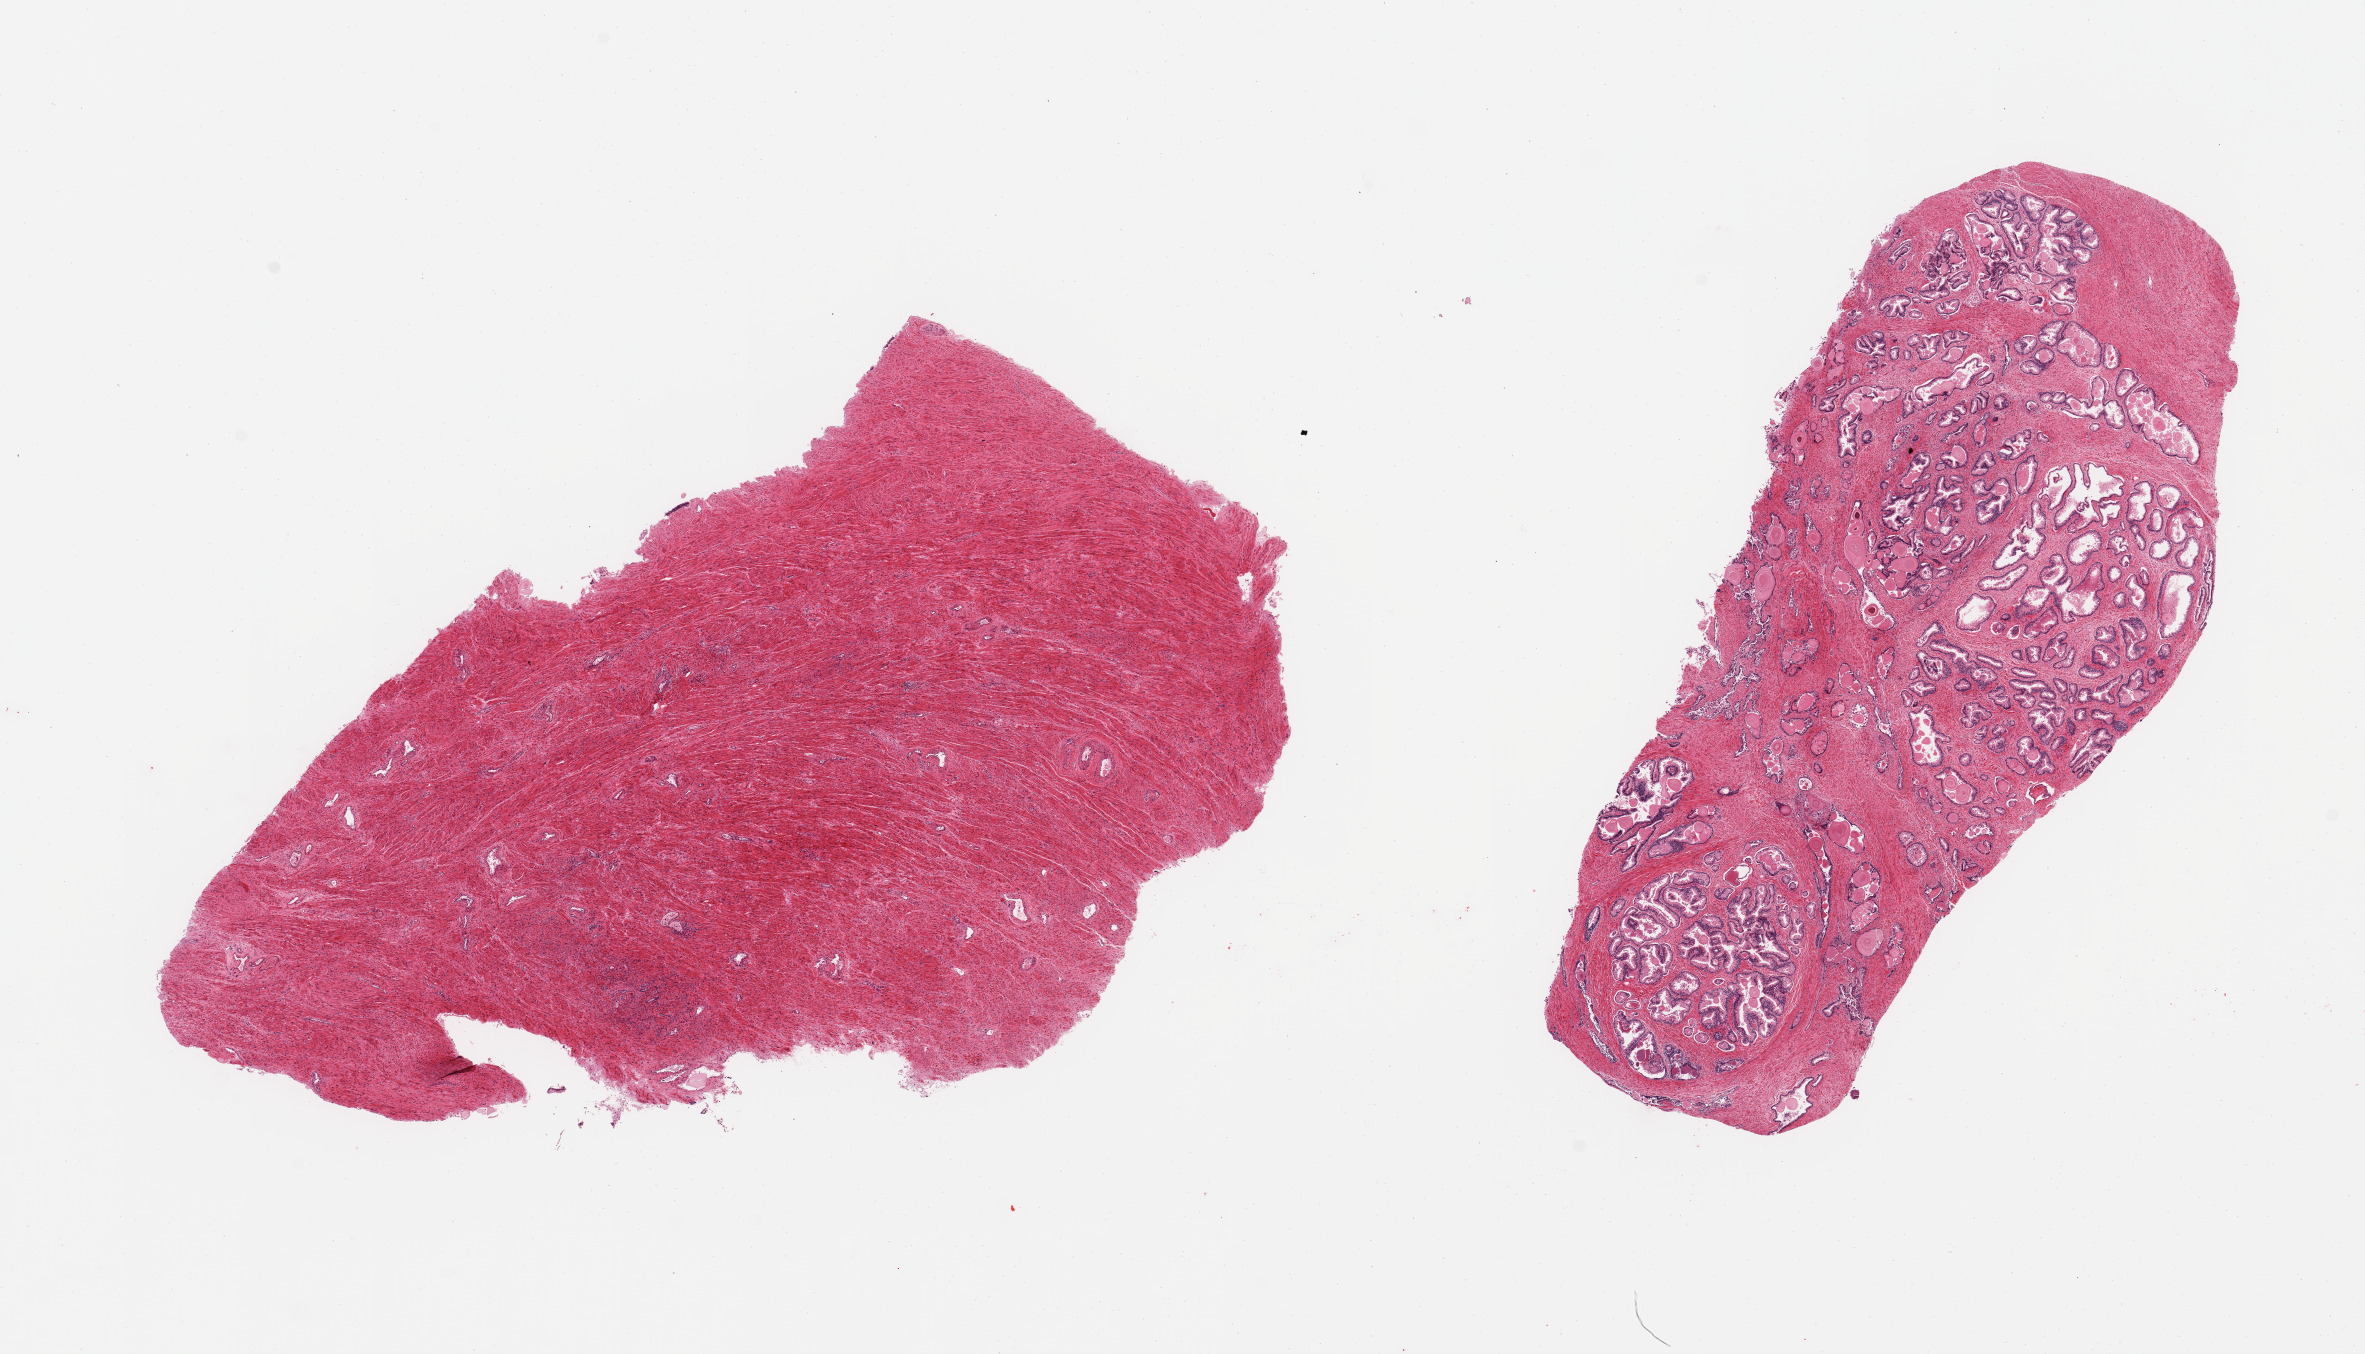
Whole-slide image, H&E stain, low-resolution overview of the scanned area, about 18.7 x 10.7 mm (slide scanned at 20x). PAXgene-fixed, paraffin-embedded tissue. Section of prostate (target tissue). Tissue donor sample. Donor sex: male.
Reviewer comment on this tissue sample: 2 pieces: 1 with nodular glandular hyperplasia, other all smooth muscle.